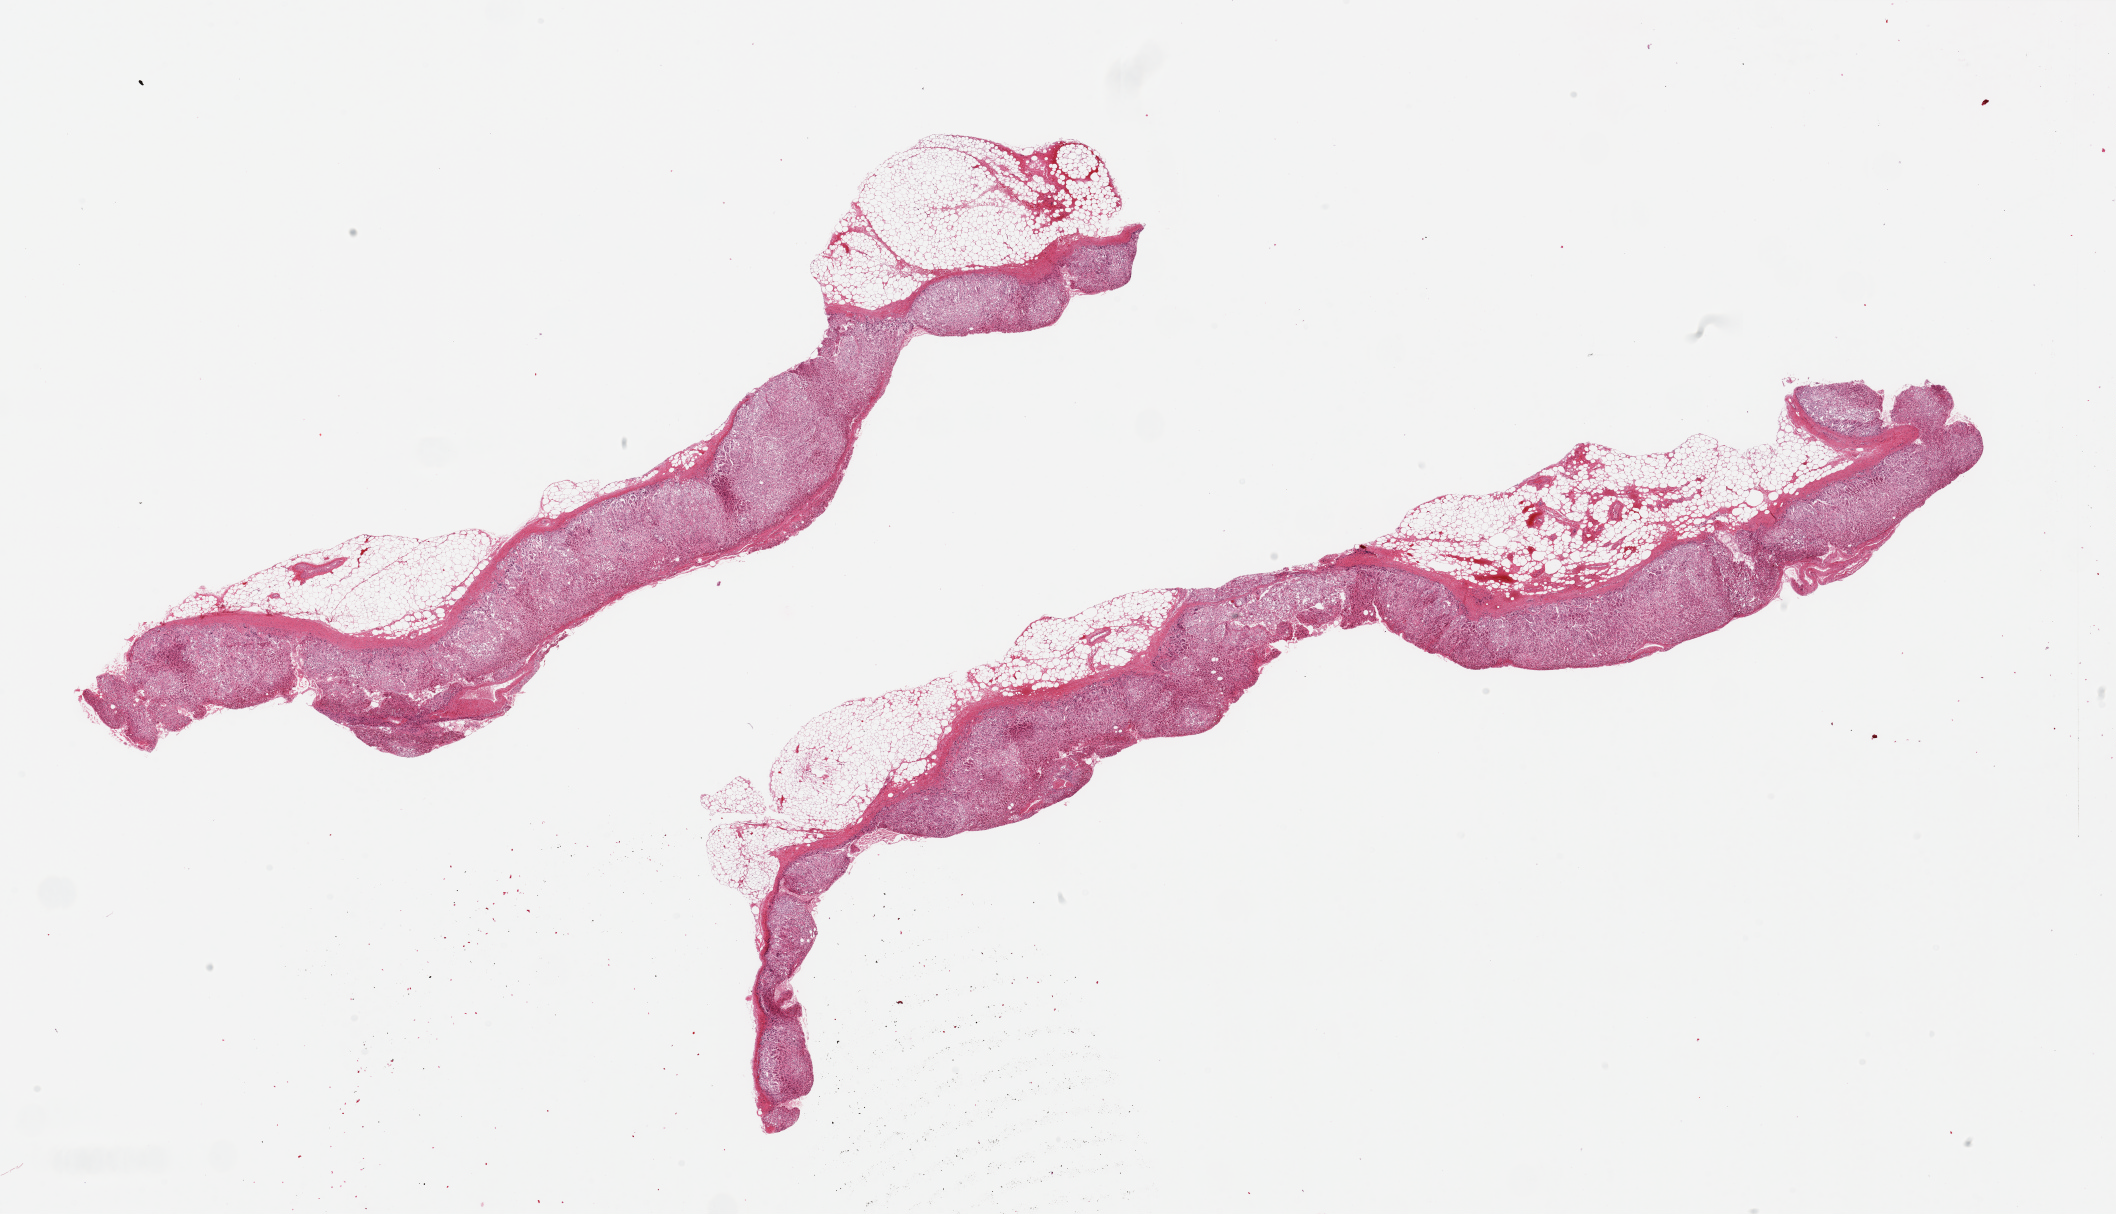
Hematoxylin and eosin (H&E) whole-slide image, brightfield — low-resolution overview of the scanned area, about 33.5 x 19.2 mm (from a 20x scan), PAXgene-fixed paraffin-embedded (PFPE) section, sampled site (target tissue): adrenal gland, donor tissue sample. Male donor.
Review note (as recorded): 2 pieces, 18x4 & 22x3.5mm; cortex; 40% peripheral adipose.